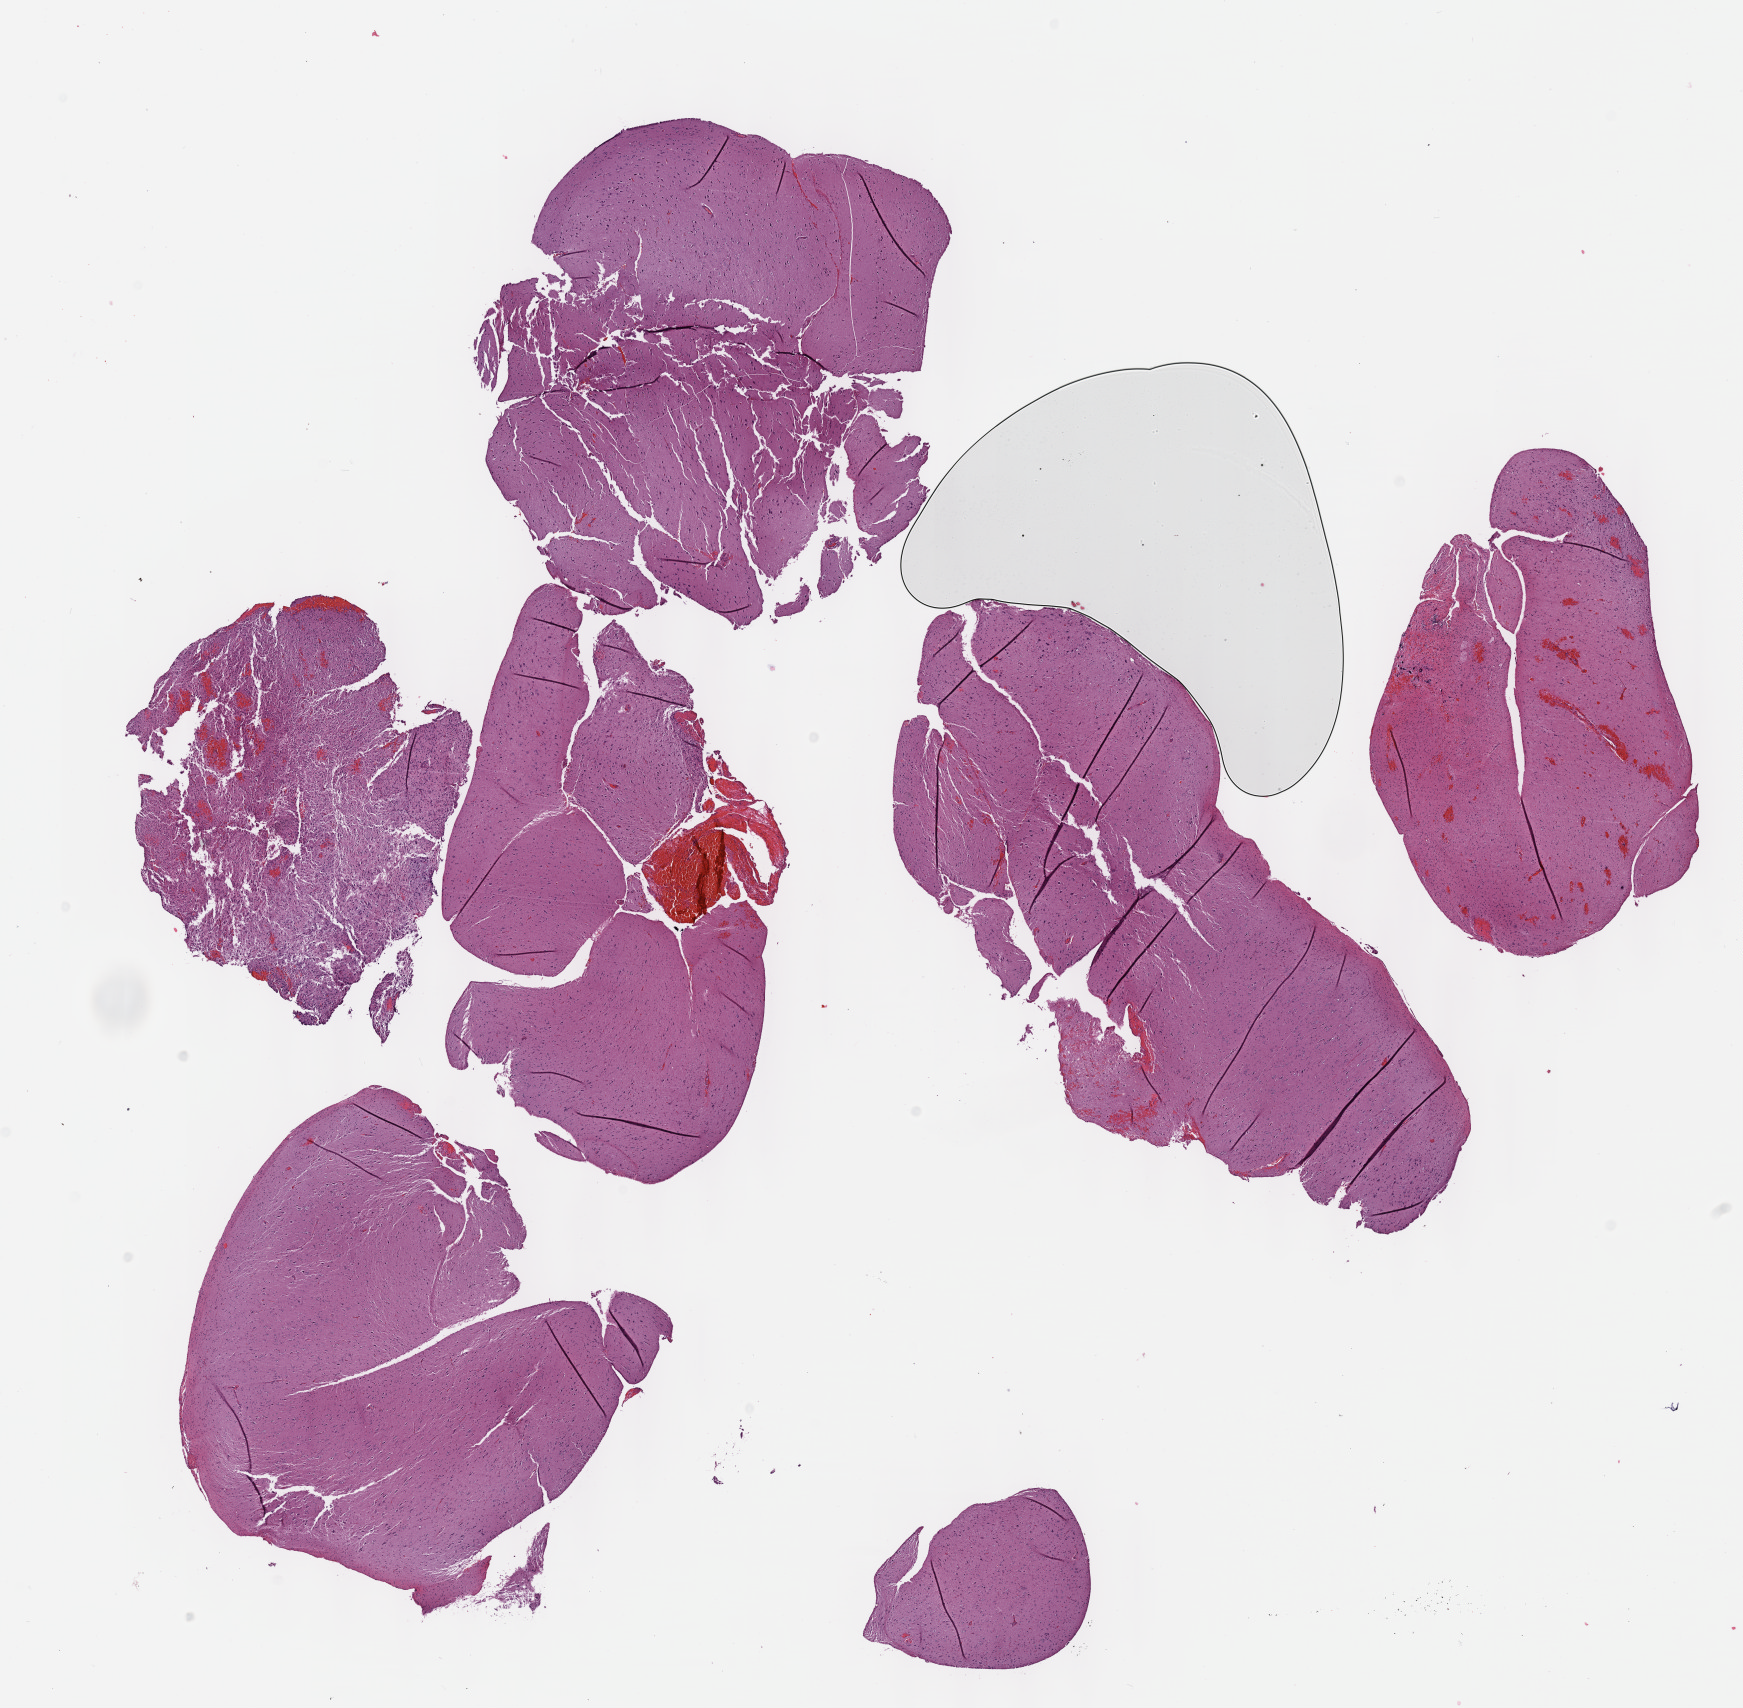
Digitized H&E tissue section (whole slide) — whole scanned area (about 14.1 x 13.8 mm) shown as a low-resolution overview, FFPE section, primary tumour sample from the brain. Patient: male, age at initial diagnosis 21 years.
Pathologic diagnosis: Astrocytoma, NOS.